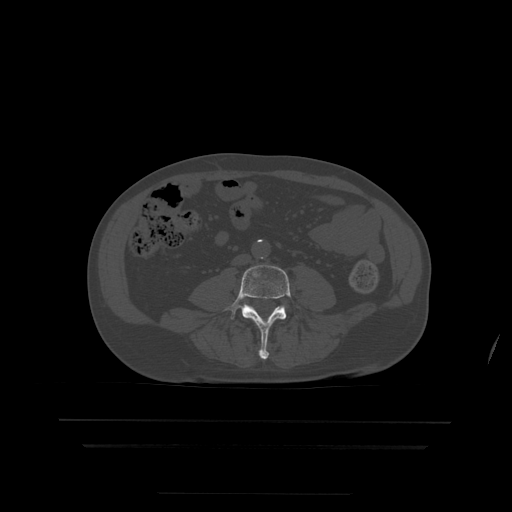
CT including the spine, one axial slice; slice 94 of 522 in the series (ordered by position); bone window (W 1800 / L 400 HU); 1.25 mm slice thickness; 512 × 512 image matrix. Patient age 68 years. From the clinical record (not read from this slice): primary cancer: urothelial.
Outlined on this slice (semi-automatically segmented with operator editing):
- L4 vertebra: bounding box (x1, y1, x2, y2) in pixels: (225, 265, 291, 360)